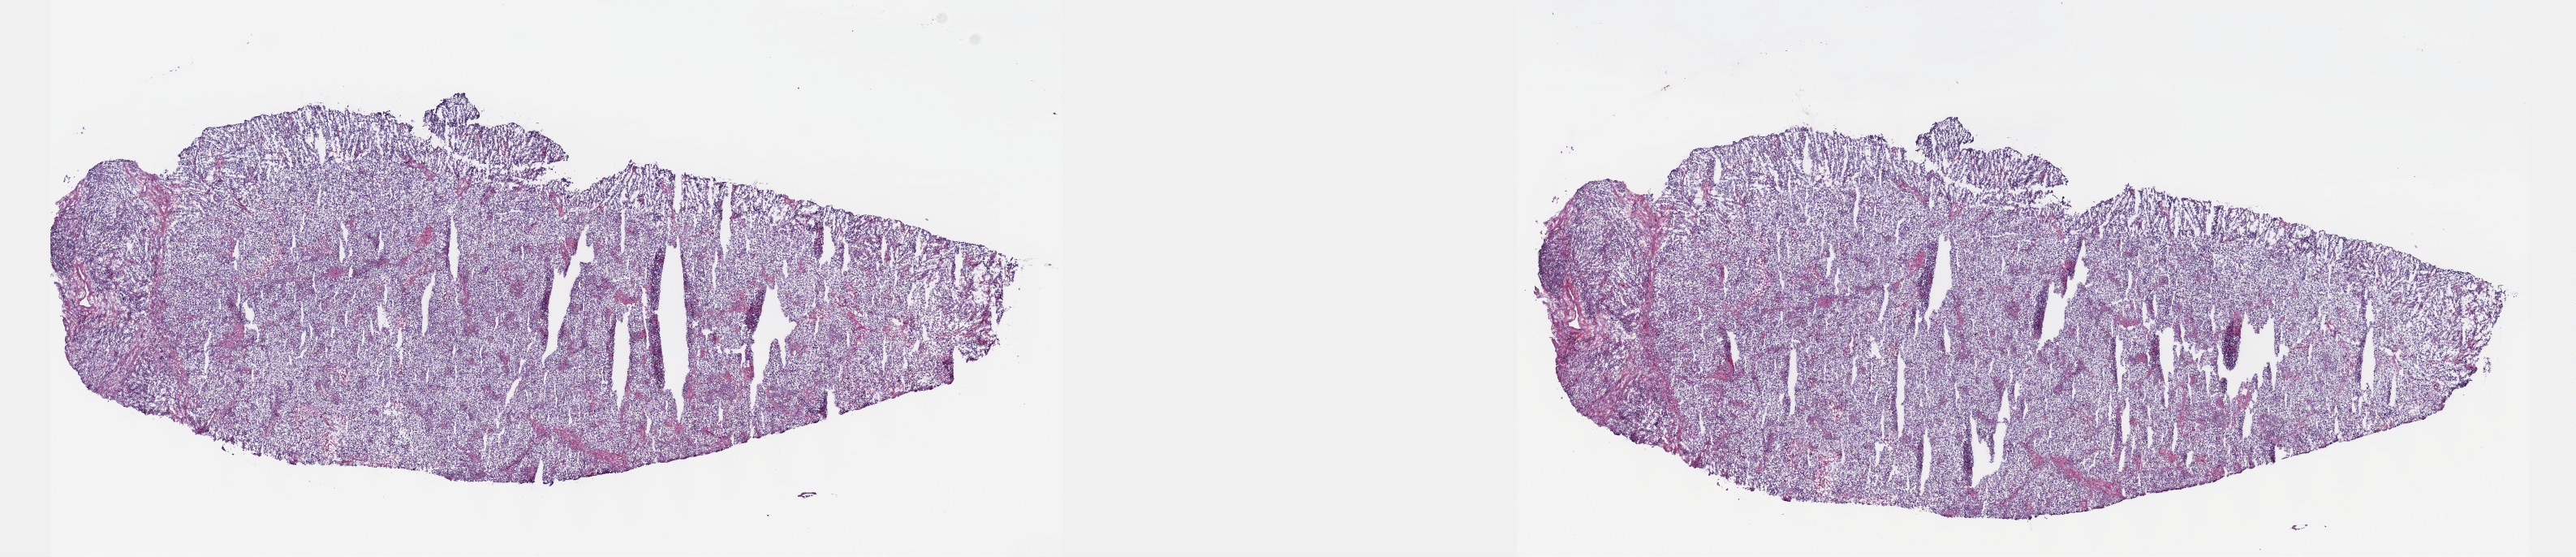
Digitized H&E-stained tissue section (whole slide), shown as a low-resolution overview of the whole scanned area (about 25.7 x 5.5 mm, acquisition: 40x scan), frozen section, testis, primary tumour sample. Male patient; age at initial diagnosis 25 years. Slide review estimates, as recorded: tumour cells 75%, tumour nuclei 75%, normal cells 0%, stromal cells 22%, necrosis 3%. Infiltration values recorded for this section: lymphocyte infiltration 6%, monocyte infiltration 1%, neutrophil infiltration 2%.
- AJCC pathologic stage: IIIB (6th edition)
- diagnosis: Seminoma, NOS
- TNM: T2 N1 M0